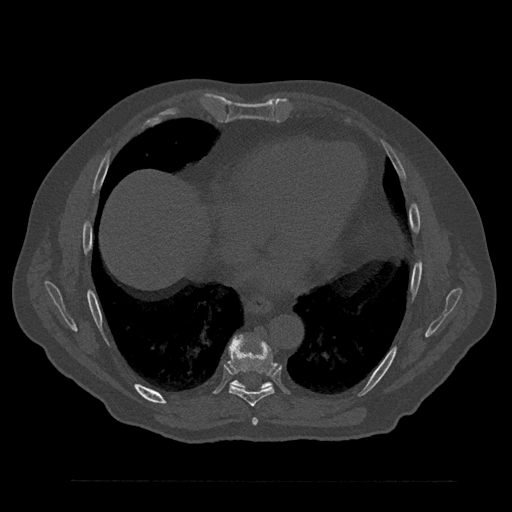
CT including the spine, one axial slice; bone window (W 1800 / L 400 HU); 0.5 mm slice thickness; 512 × 512 image matrix, field of view 430 × 430 mm. Male patient, age 61 years. From the clinical record (not read from this slice): primary cancer: prostate.
Outlined on this slice (semi-automatically segmented with operator editing):
- T7 vertebra: box from (x=252, y=418) to (x=258, y=425) px
- T8 vertebra: (x=228, y=336)–(x=278, y=406)
- T9 vertebra: (x=231, y=380)–(x=272, y=389)